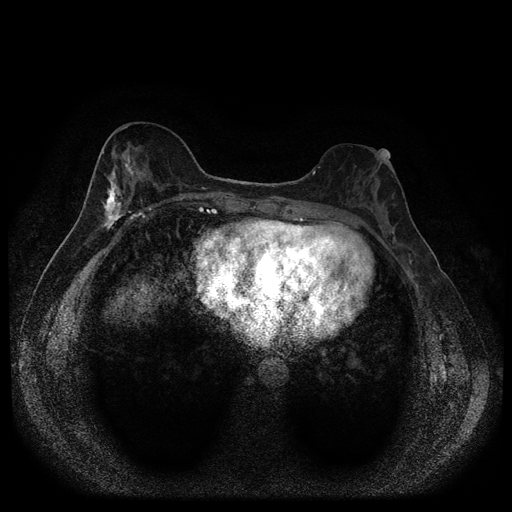
Breast MRI (dynamic contrast-enhanced, multi-phase), one axial slice. Slice 41 of 116 in the series (ordered by position). Dynamic contrast-enhanced series, time point 2 of 5 at this slice position (early post-contrast). 1.5 T. TE 2.7 ms, TR 5.4 ms. 2 mm slice thickness. 512 × 512 image matrix. Female patient, age 49 years.
Annotated regions visible in this slice (semi-automatically segmented with operator editing):
- breast lesion (labelled 'tumour' in the annotation; benign lesions carry a separate 'benign' label): bounding box <98,151,136,235> (left, top, right, bottom; pixels)